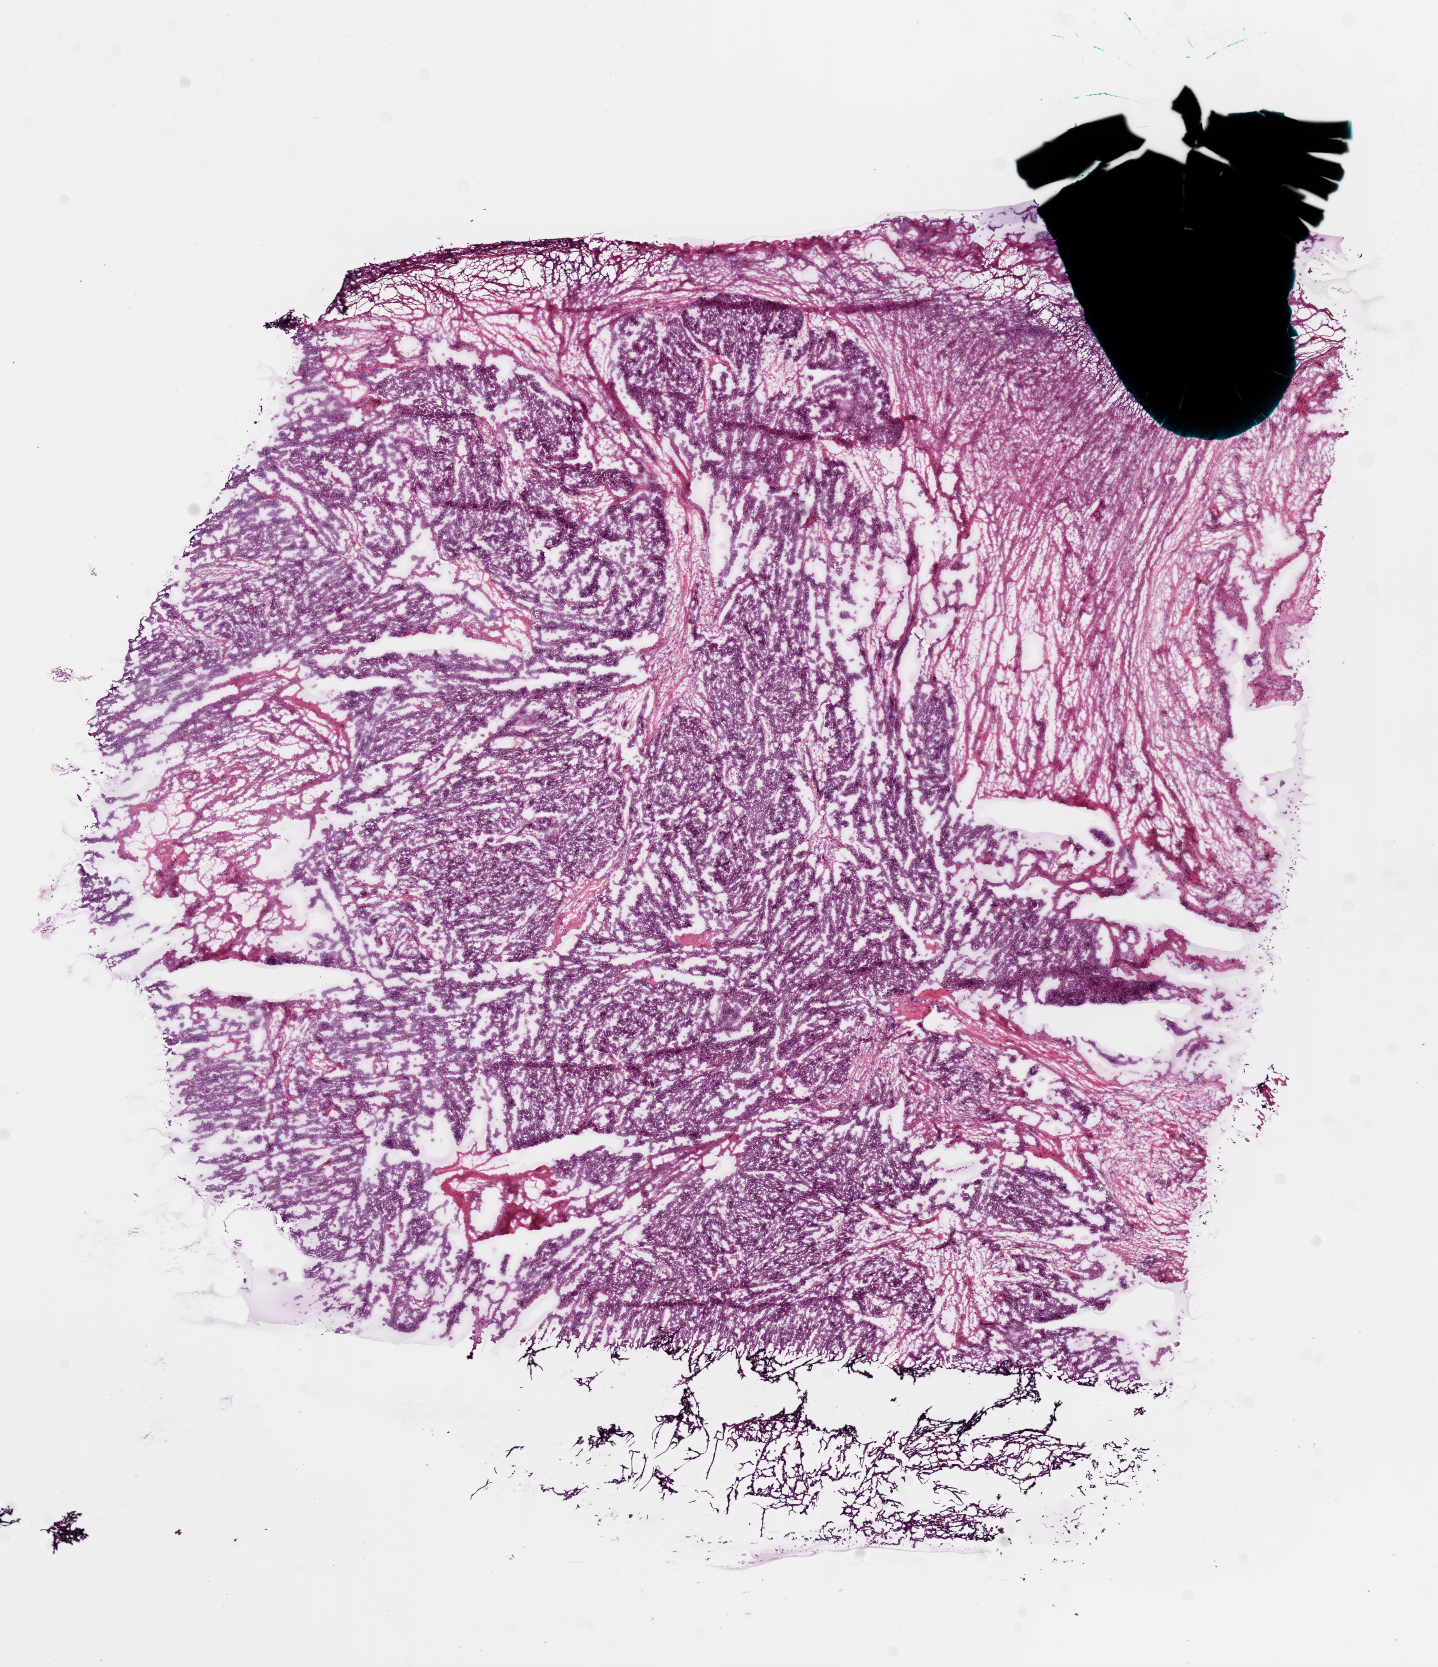
H&E-stained whole-slide image, a low-resolution overview of the entire scanned area, about 11.6 x 13.5 mm (slide scanned at 20x); frozen section from the bottom of the tissue portion; primary tumour sample from the ovary. Female, age 69 years at initial diagnosis. Histologic grade: G3 (poorly differentiated). Pathologist review of this section (percent, as recorded): tumour cells 79%, tumour nuclei 90%, normal cells 0%, stromal cells 20%, necrosis 1%.
Diagnosis: Serous cystadenocarcinoma, NOS. FIGO stage: IV.